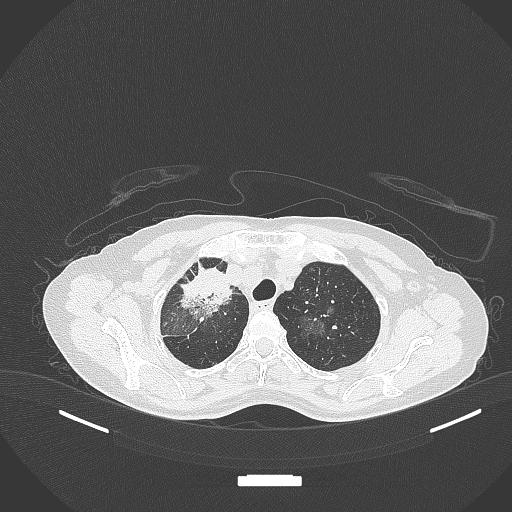
Chest CT, one axial slice. Slice 269 of 284 in the series (ordered by position). 120 kVp. Lung window (W 1500 / L -600 HU). 1 mm slice thickness. 512 × 512 image matrix, field of view 400 × 400 mm. Female patient, age 59 years. Case-level facts recorded for this patient, not image findings: clinical TNM (as recorded): T3 N0 M0.
Structures marked on this image (rectangle marked by the reading radiologist):
- lung tumour (recorded histology: adenocarcinoma): bounding box [x1, y1, x2, y2] px = [175, 257, 233, 321]